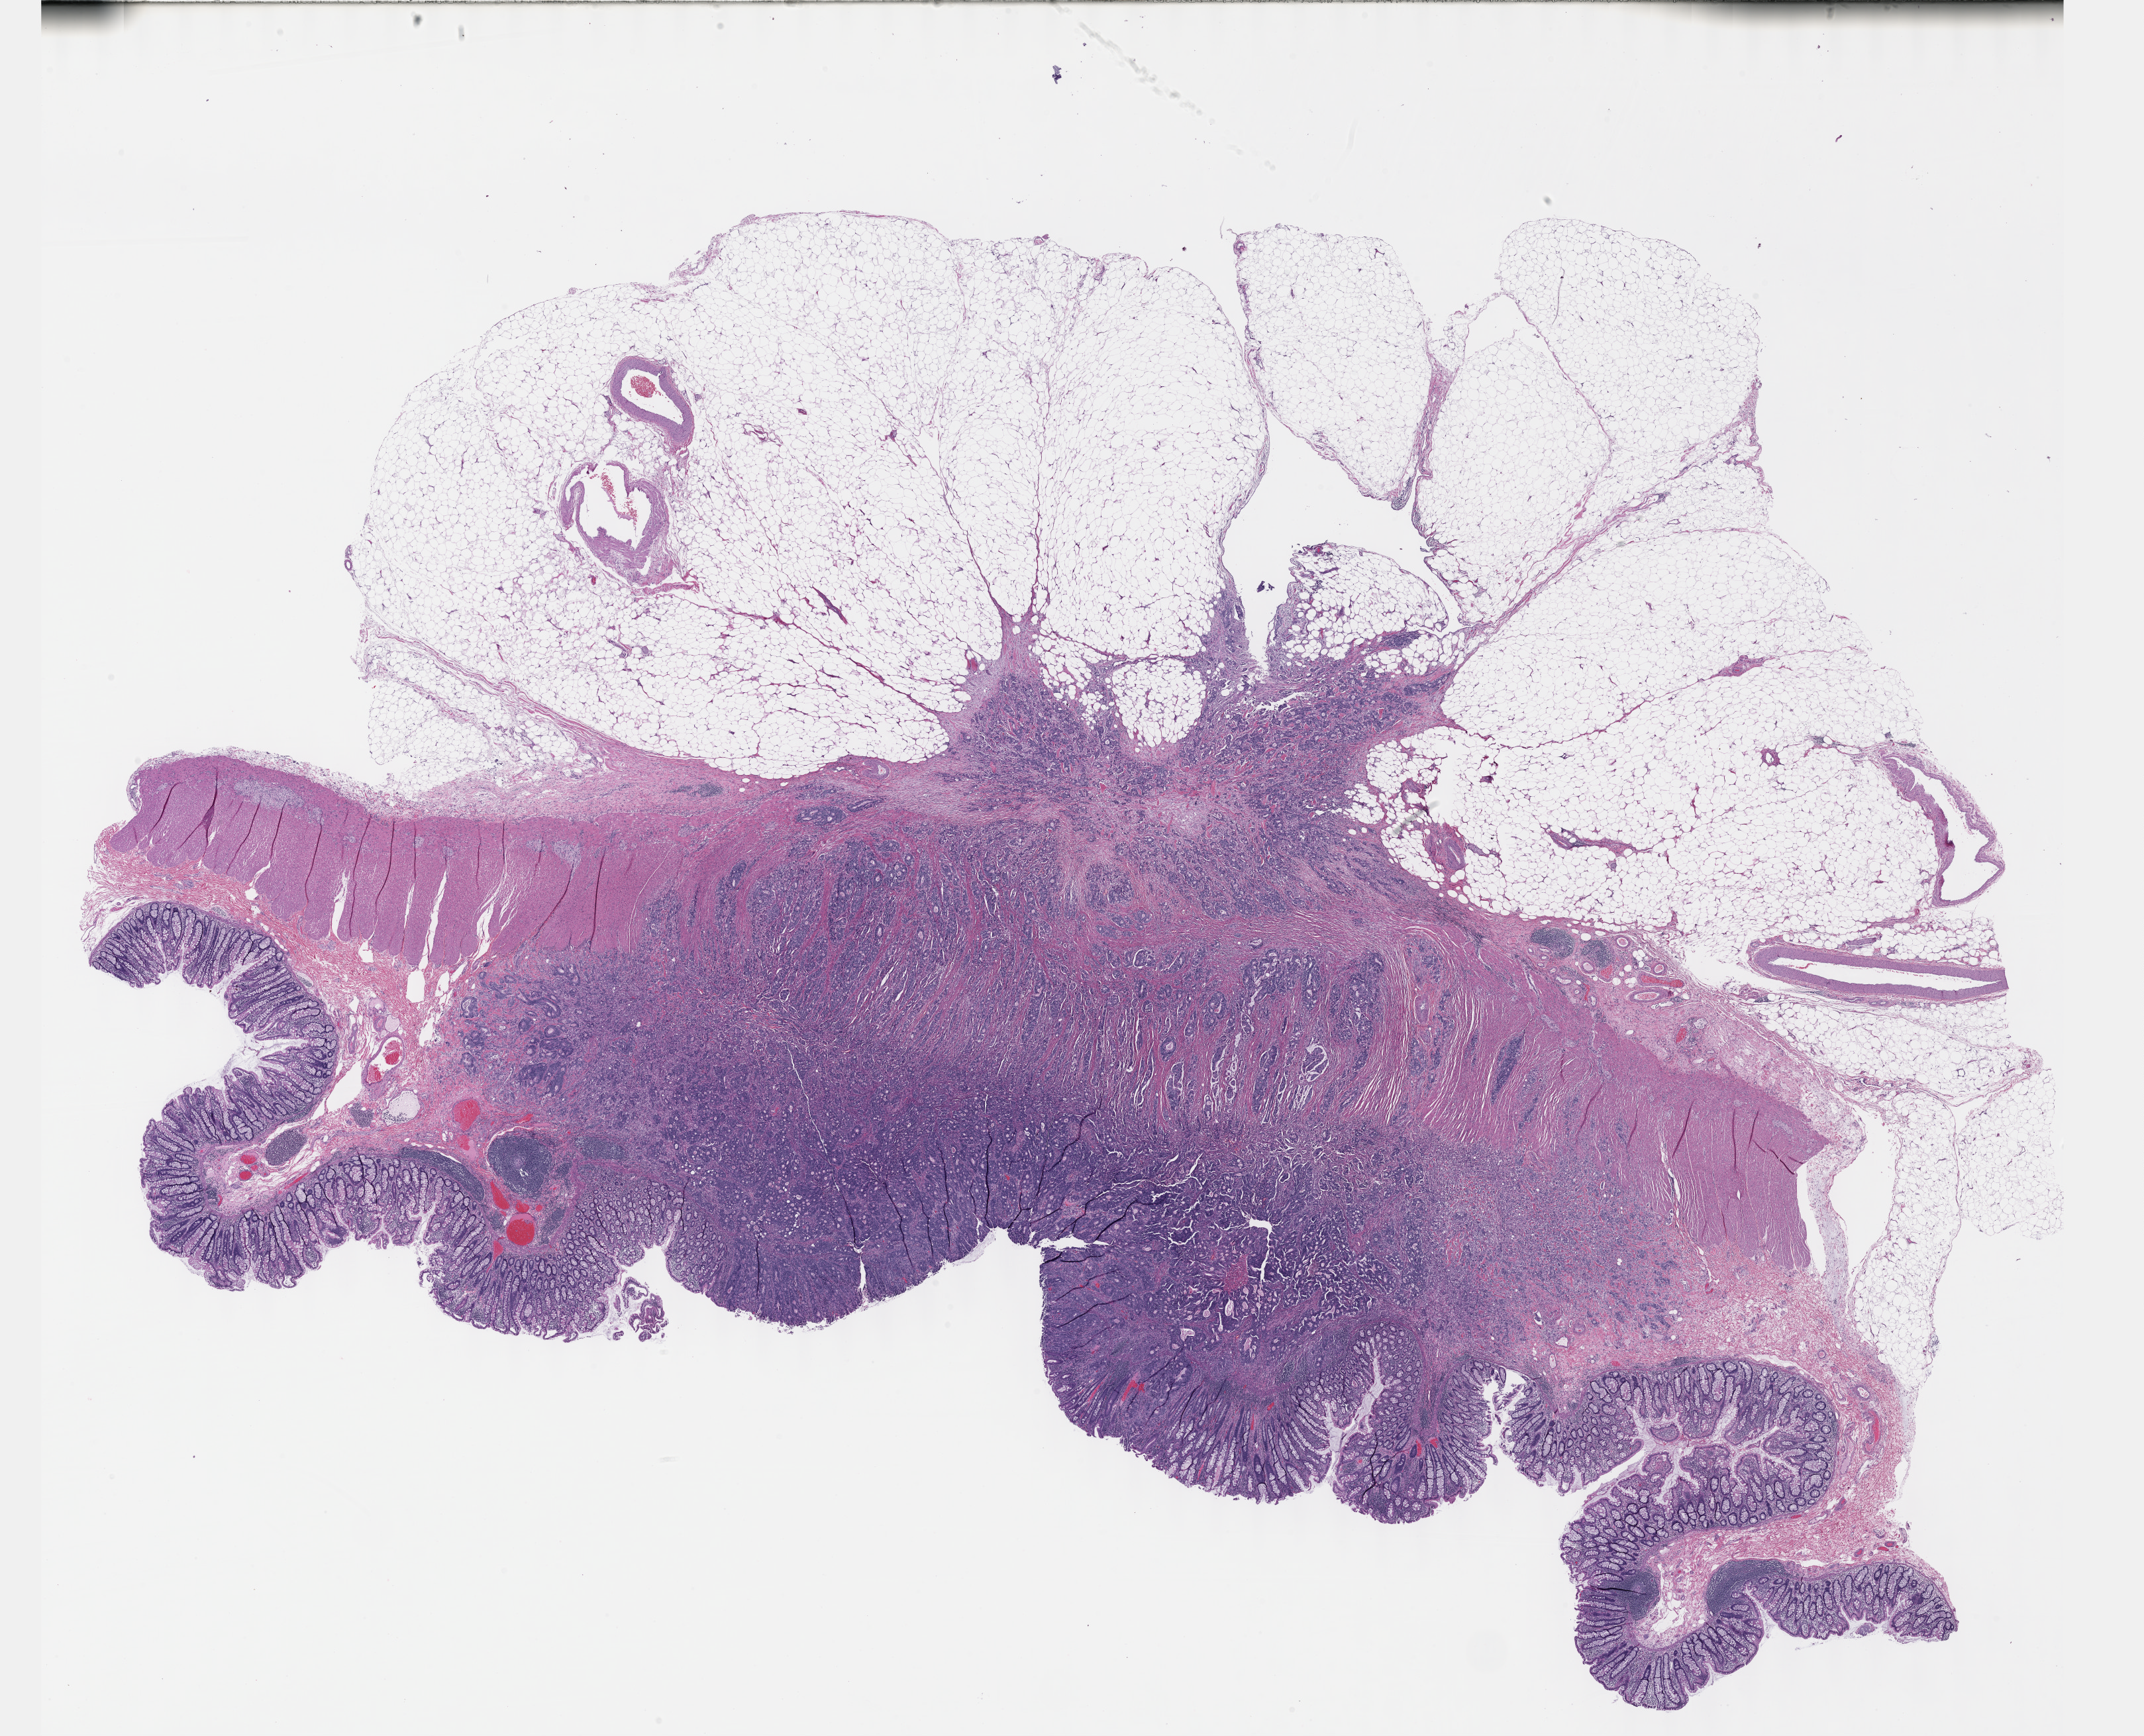
Whole-slide histology image, H&E — a low-resolution overview of the entire scanned area, about 26.2 x 21.2 mm (slide scanned at 40x), formalin-fixed paraffin-embedded (FFPE) diagnostic section, colon, primary tumour sample. Male patient; age at initial diagnosis 58 years.
Lymph nodes positive (case pathology): 4 of 33 examined. AJCC pathologic stage: IIIC (7th edition). Pathologic diagnosis: Adenocarcinoma, NOS (ascending colon).